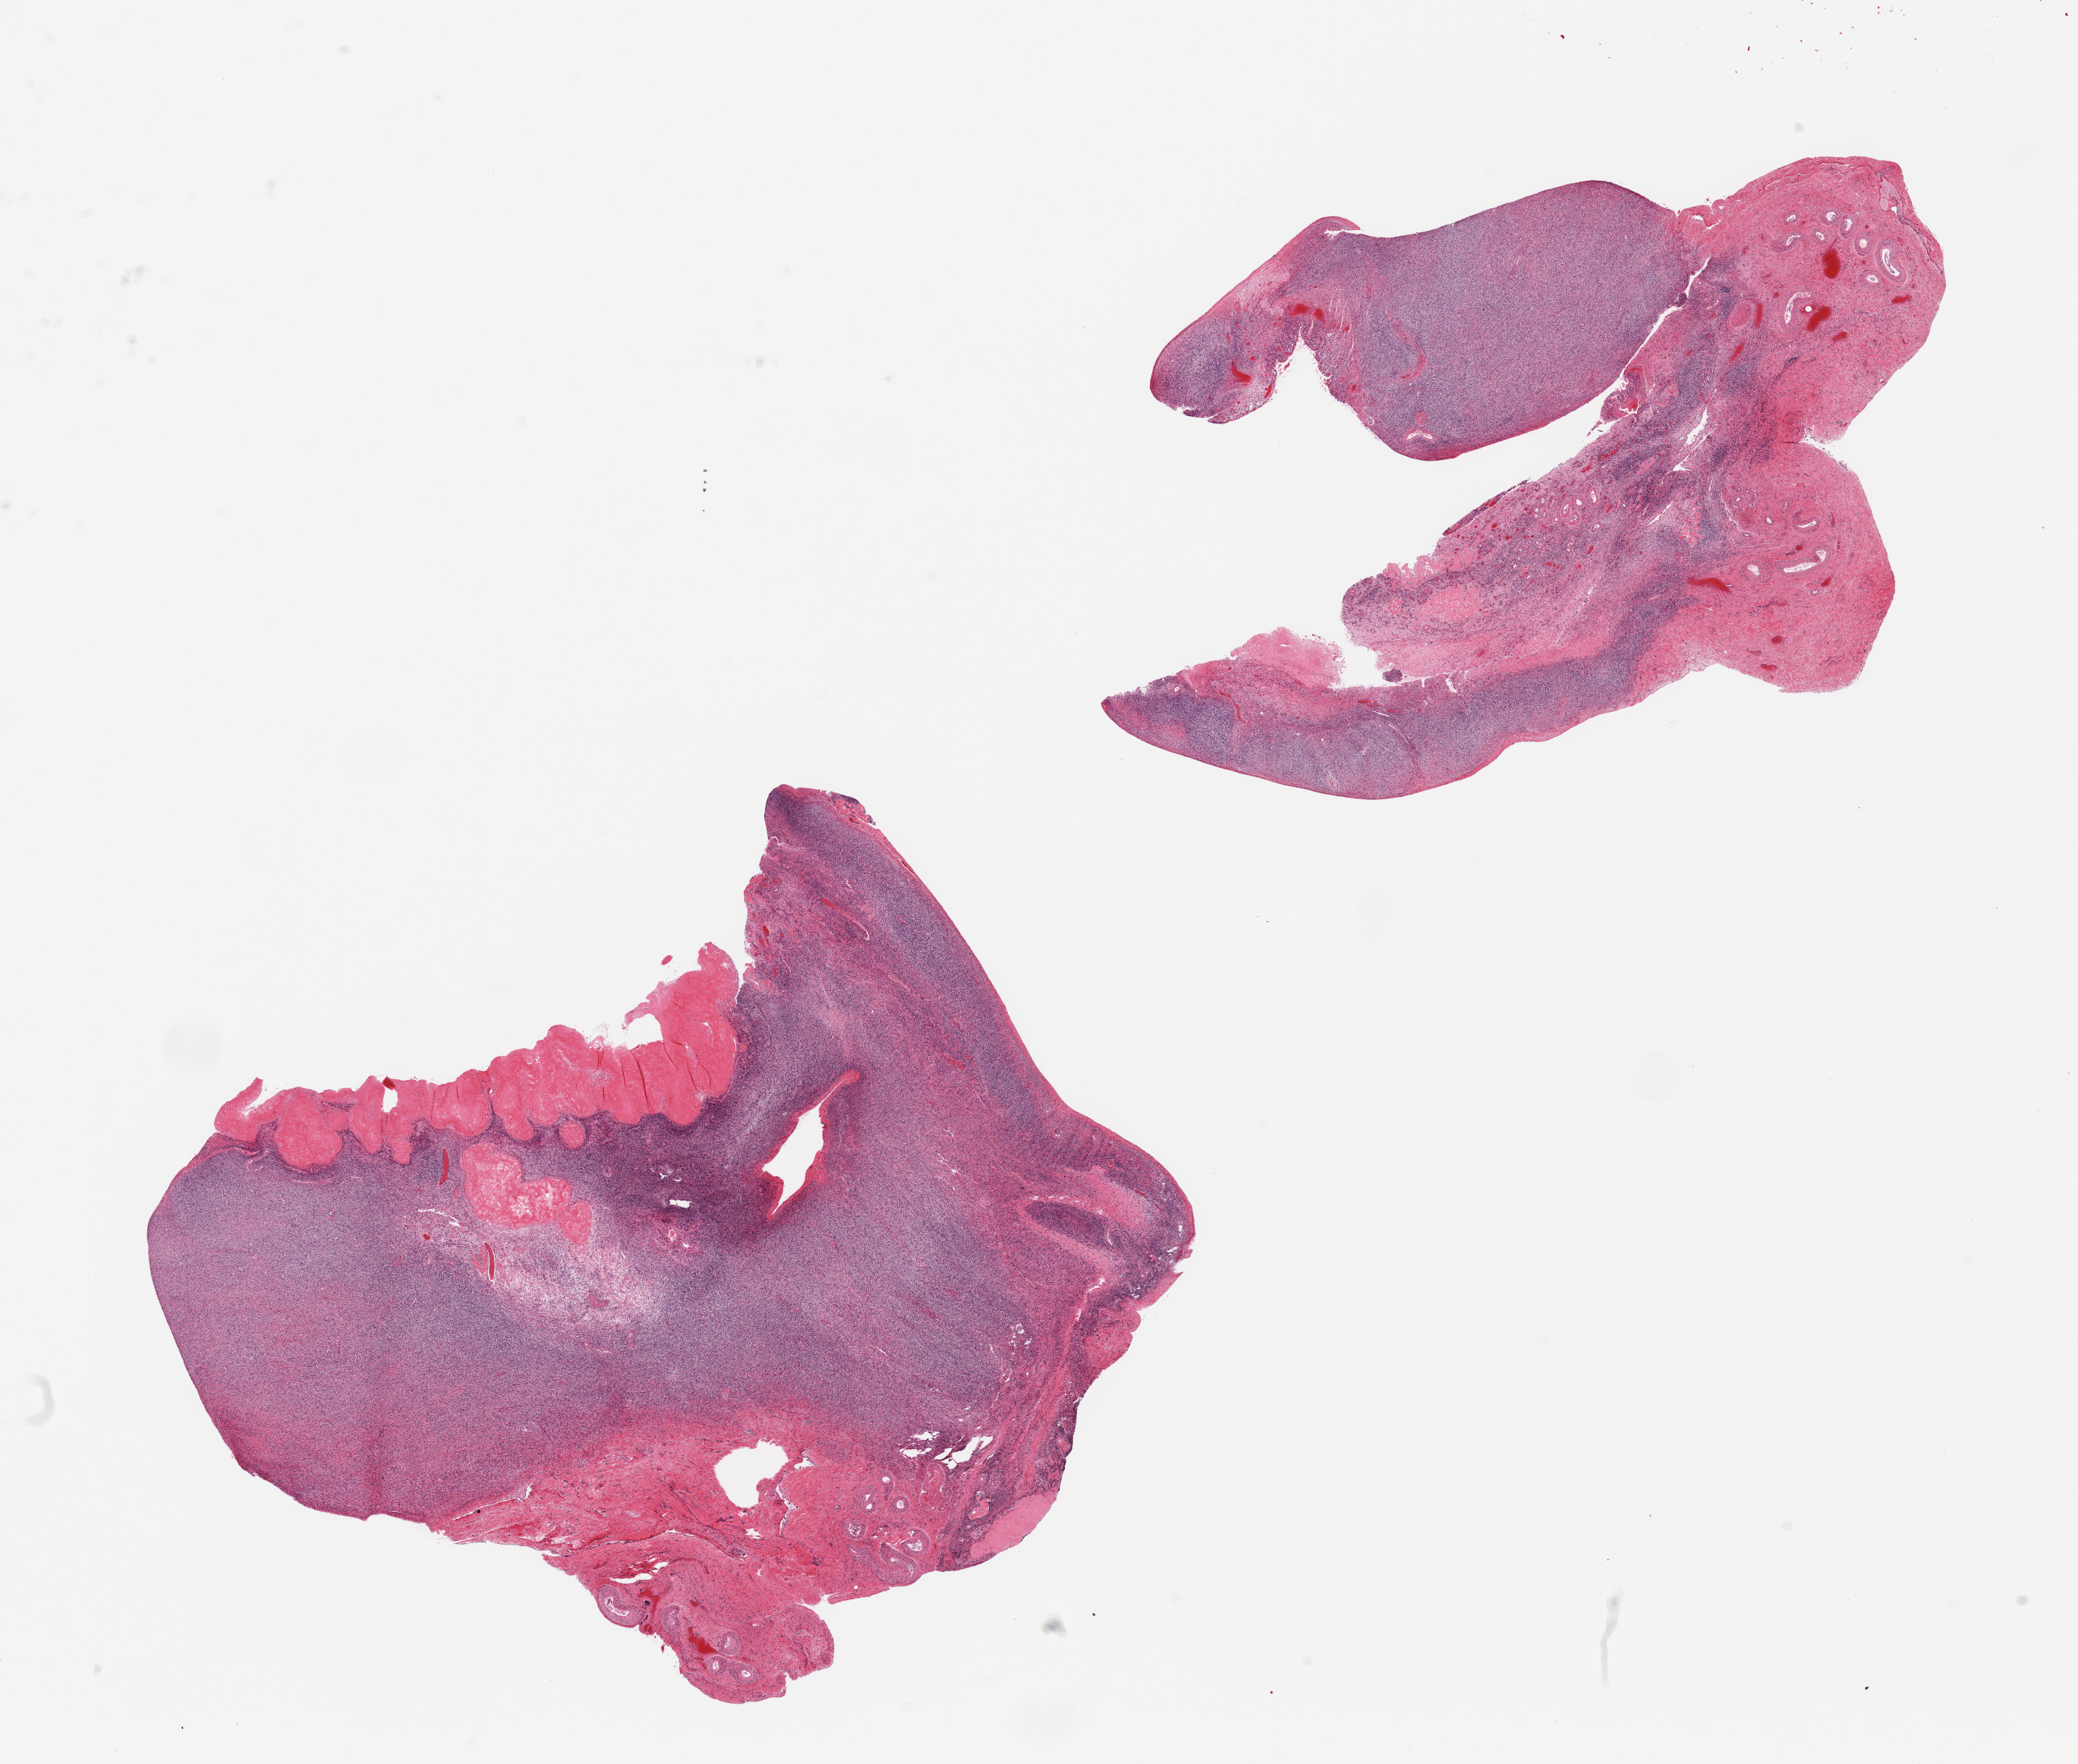
Whole-slide image, haematoxylin and eosin stain, whole scanned area (about 21.7 x 18.4 mm) shown as a low-resolution overview, PAXgene-fixed paraffin-embedded (PFPE) section, sampled site (target tissue): ovary, donor tissue sample. Donor: female.
* pathologist's review note for this sample: 2 pieces, typical post-menopausal atrophy, no abnormalities